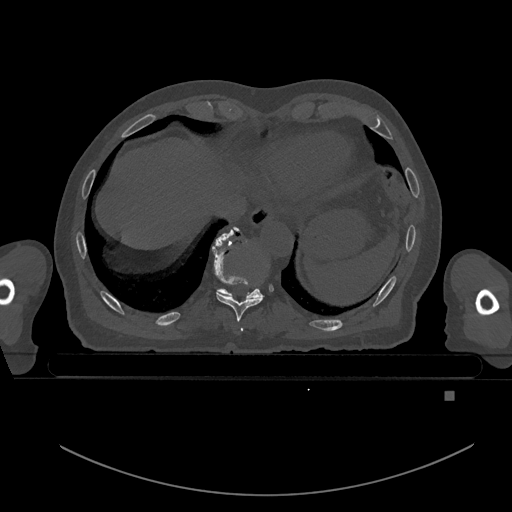
CT including the spine, one axial slice; position 128 of 969 along the scan axis; bone window (W 1800 / L 400 HU); 512 × 512 image matrix, field of view 456 × 456 mm. Male patient, age 82 years. From the clinical record (not read from this slice): primary cancer: prostate; vertebrae with lytic lesions (as recorded): T11, T9, T8, T2.
Structures marked on this image (semi-automatically segmented with operator editing):
- T10 vertebra: bounding box <219,227,261,298> (left, top, right, bottom; pixels)
- T9 vertebra: <212,230,264,330>